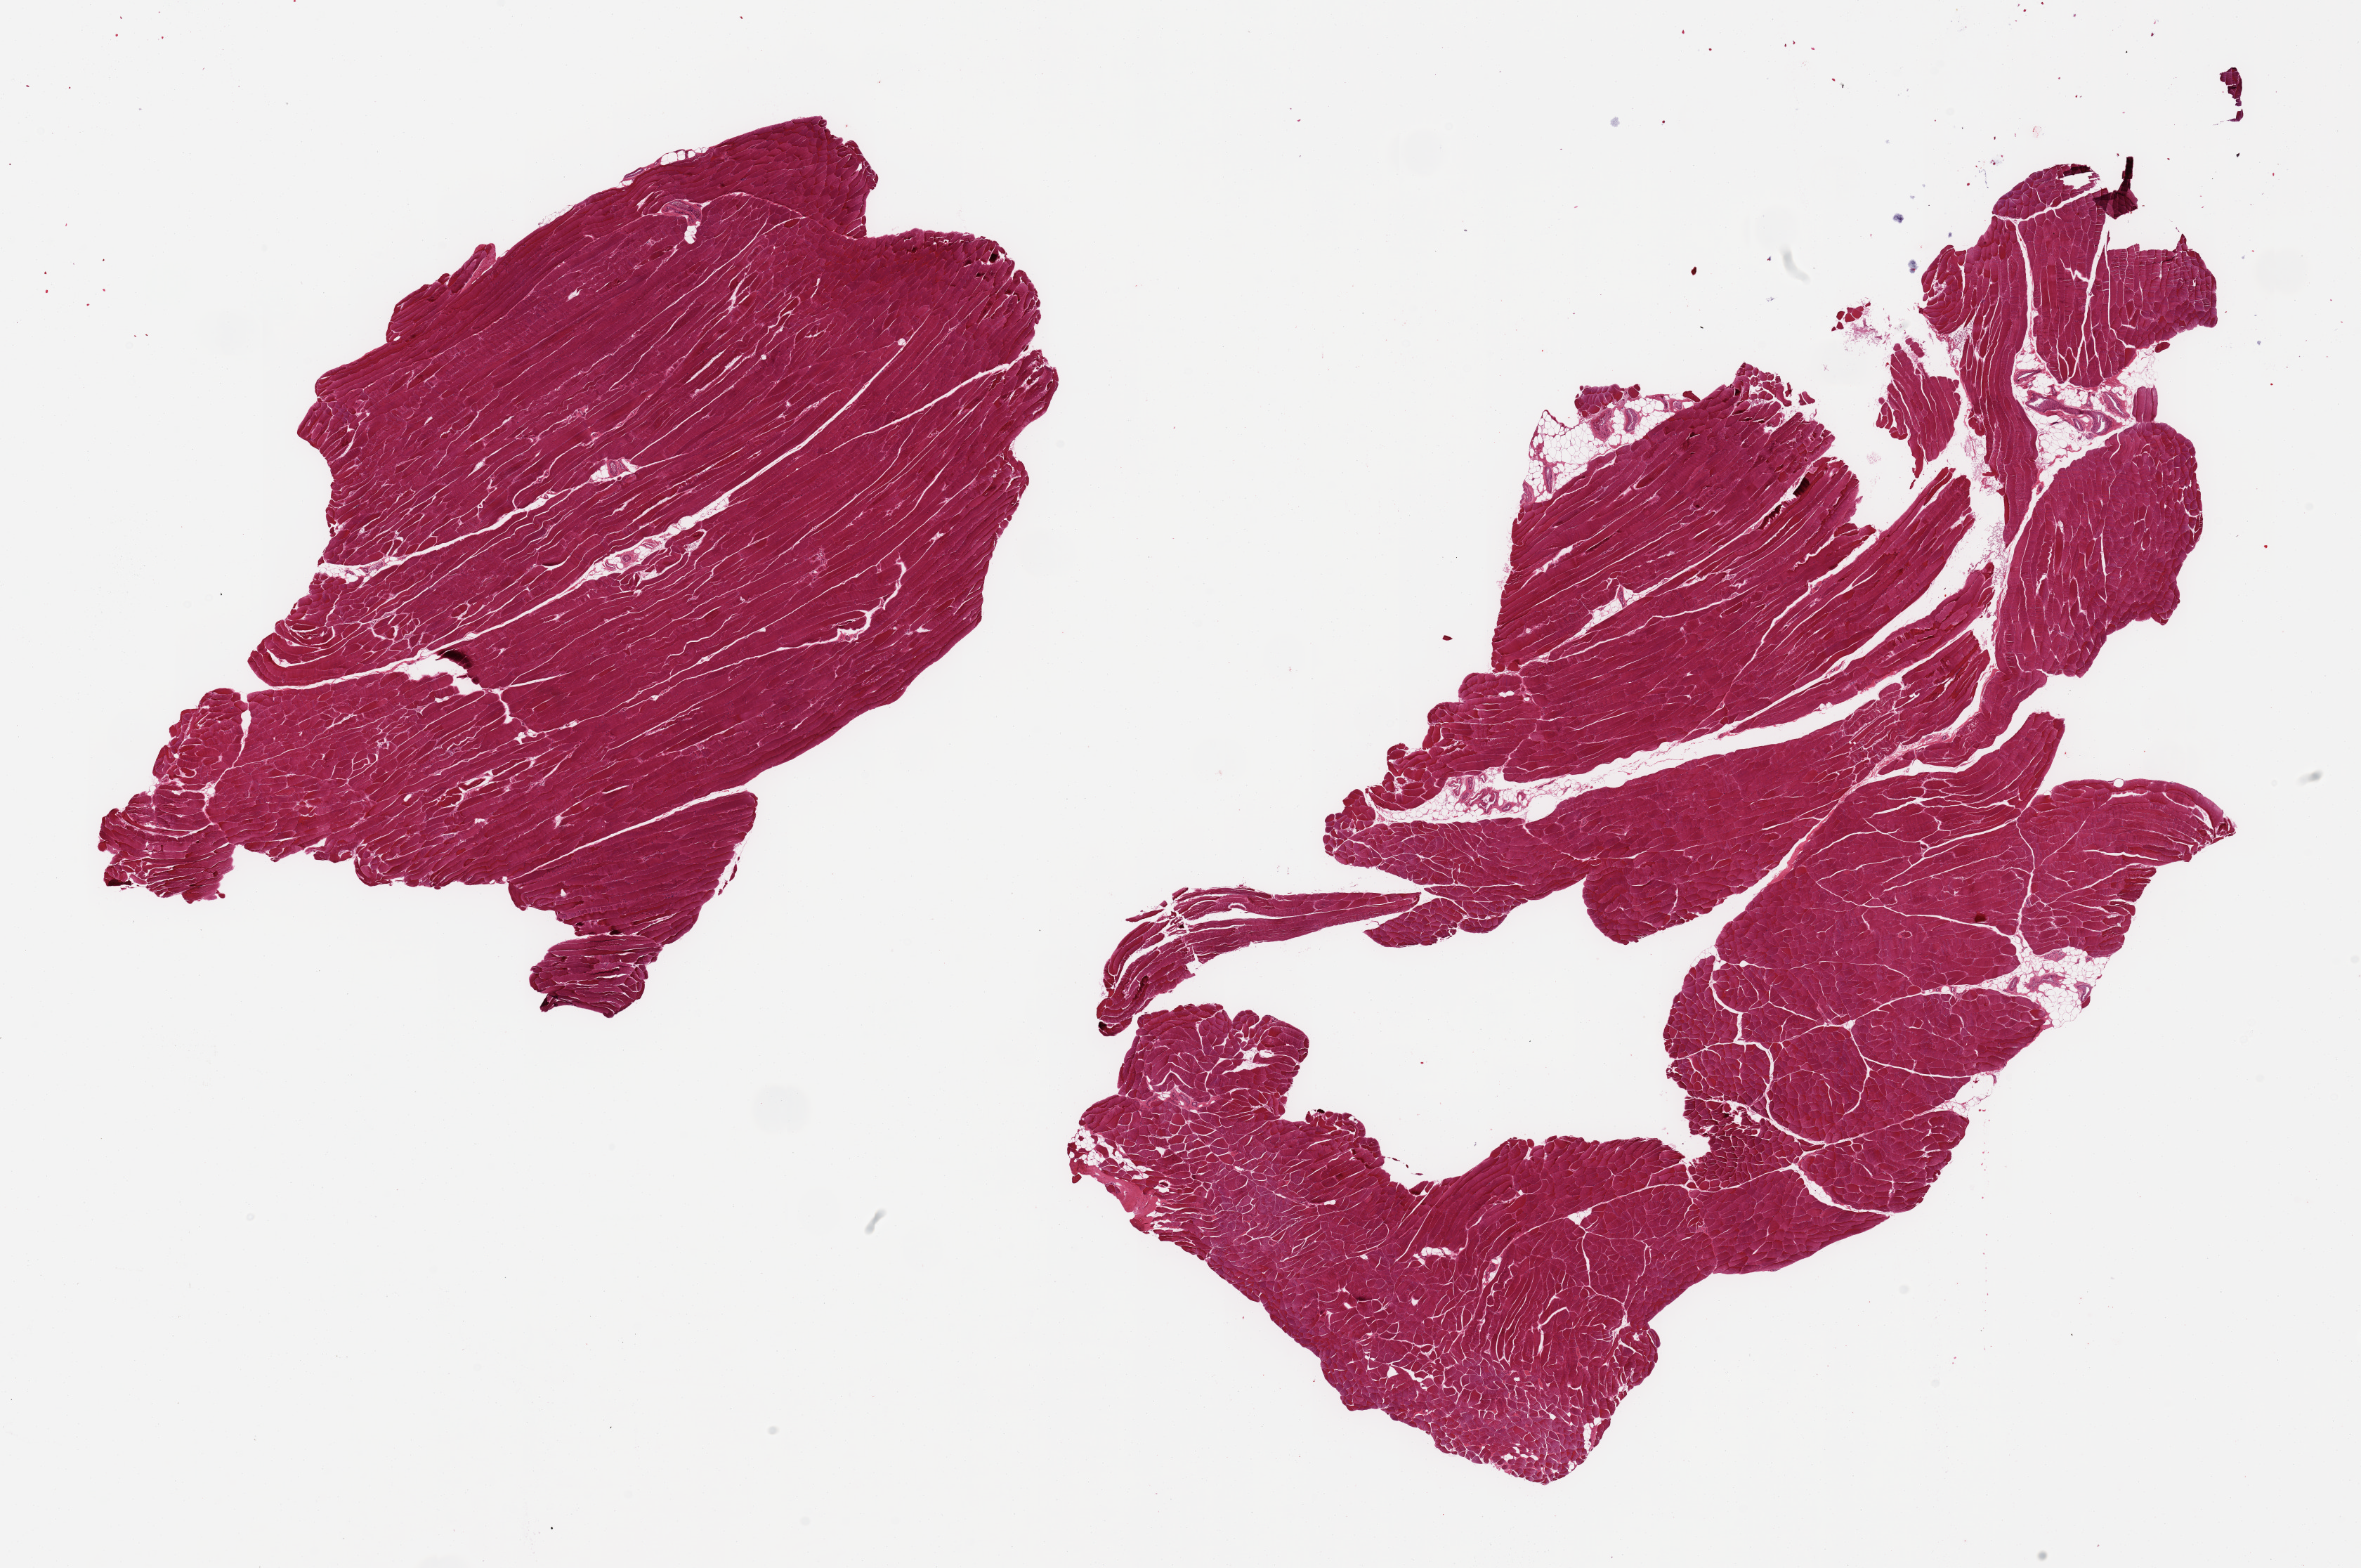
Whole-slide image, haematoxylin and eosin stain — a low-resolution overview of the entire scanned area, about 26.6 x 17.7 mm (from a 20x scan); PAXgene-fixed, paraffin-embedded tissue; target tissue: skeletal muscle; donor tissue sample. Donor sex: male.
* pathologist's review note for this sample: 2 pieces; 2% internal fat